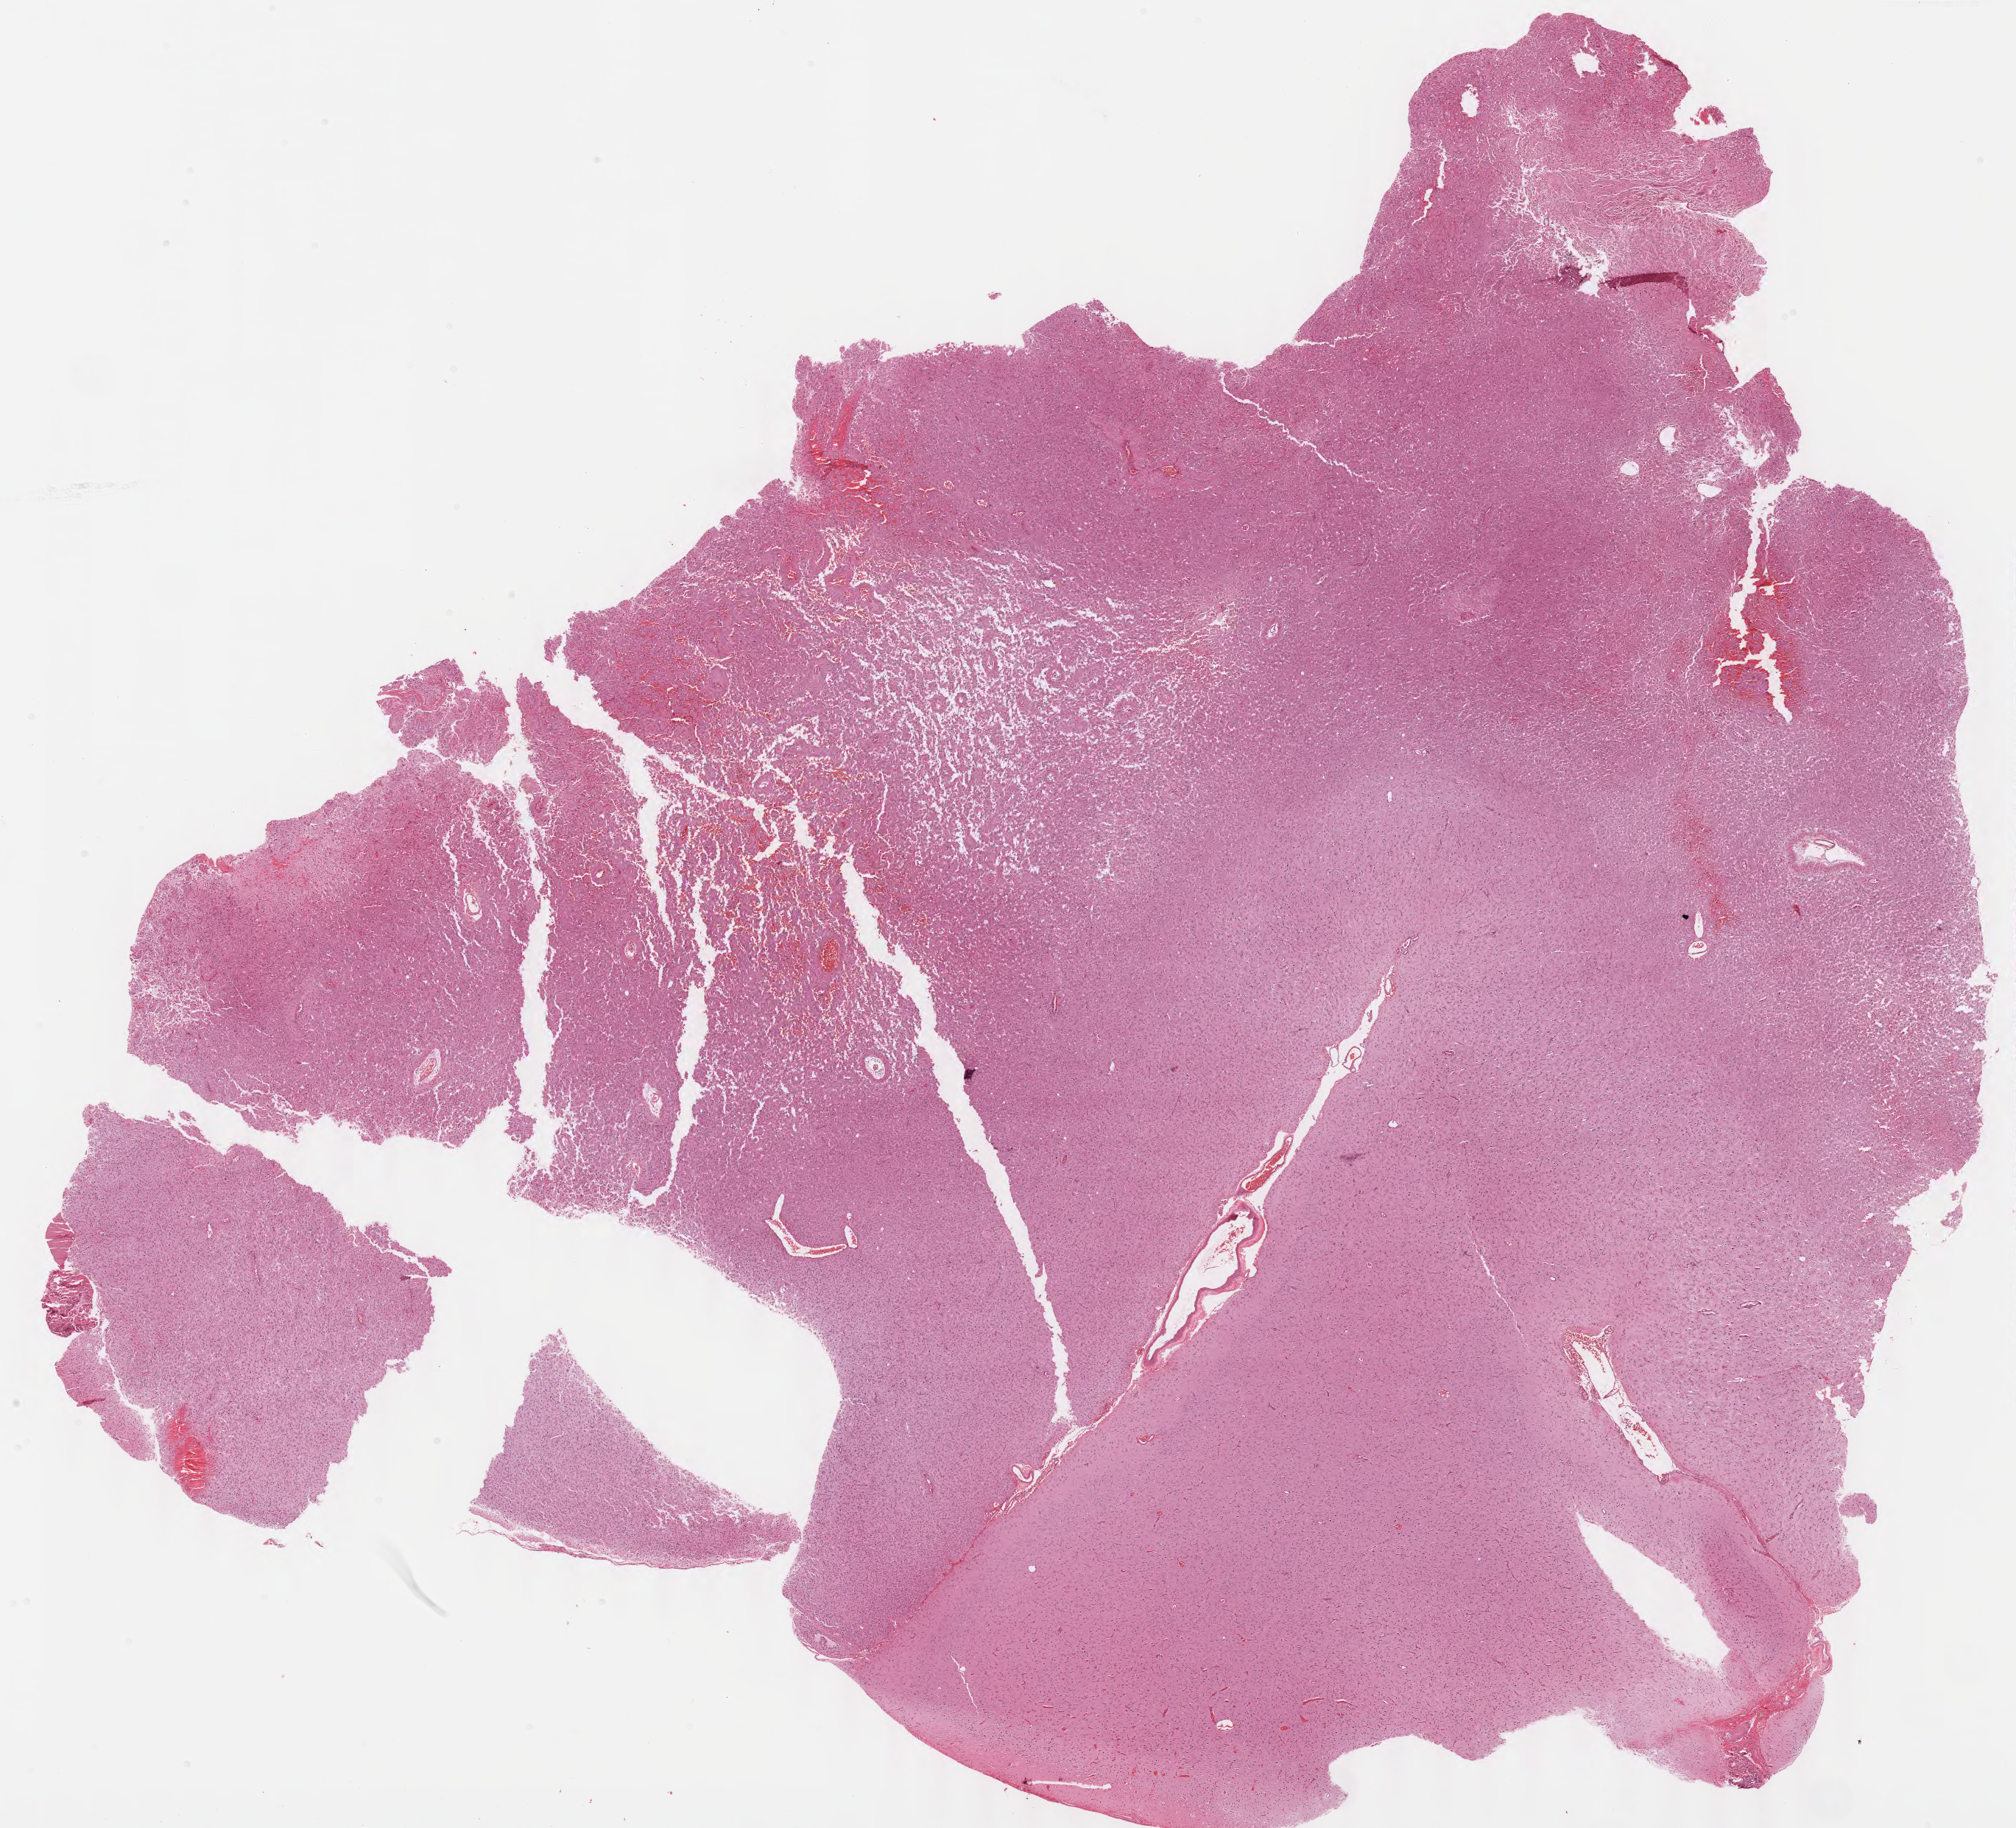
Whole-slide histology image, H&E — shown as a low-resolution overview of the whole scanned area (about 21.6 x 19.6 mm, acquisition: 40x scan). Formalin-fixed paraffin-embedded (FFPE) diagnostic section. Sample: primary tumour, brain. Patient: male, age at initial diagnosis 59 years. Histologic grade: G2 (moderately differentiated).
Pathologic diagnosis: Mixed glioma.